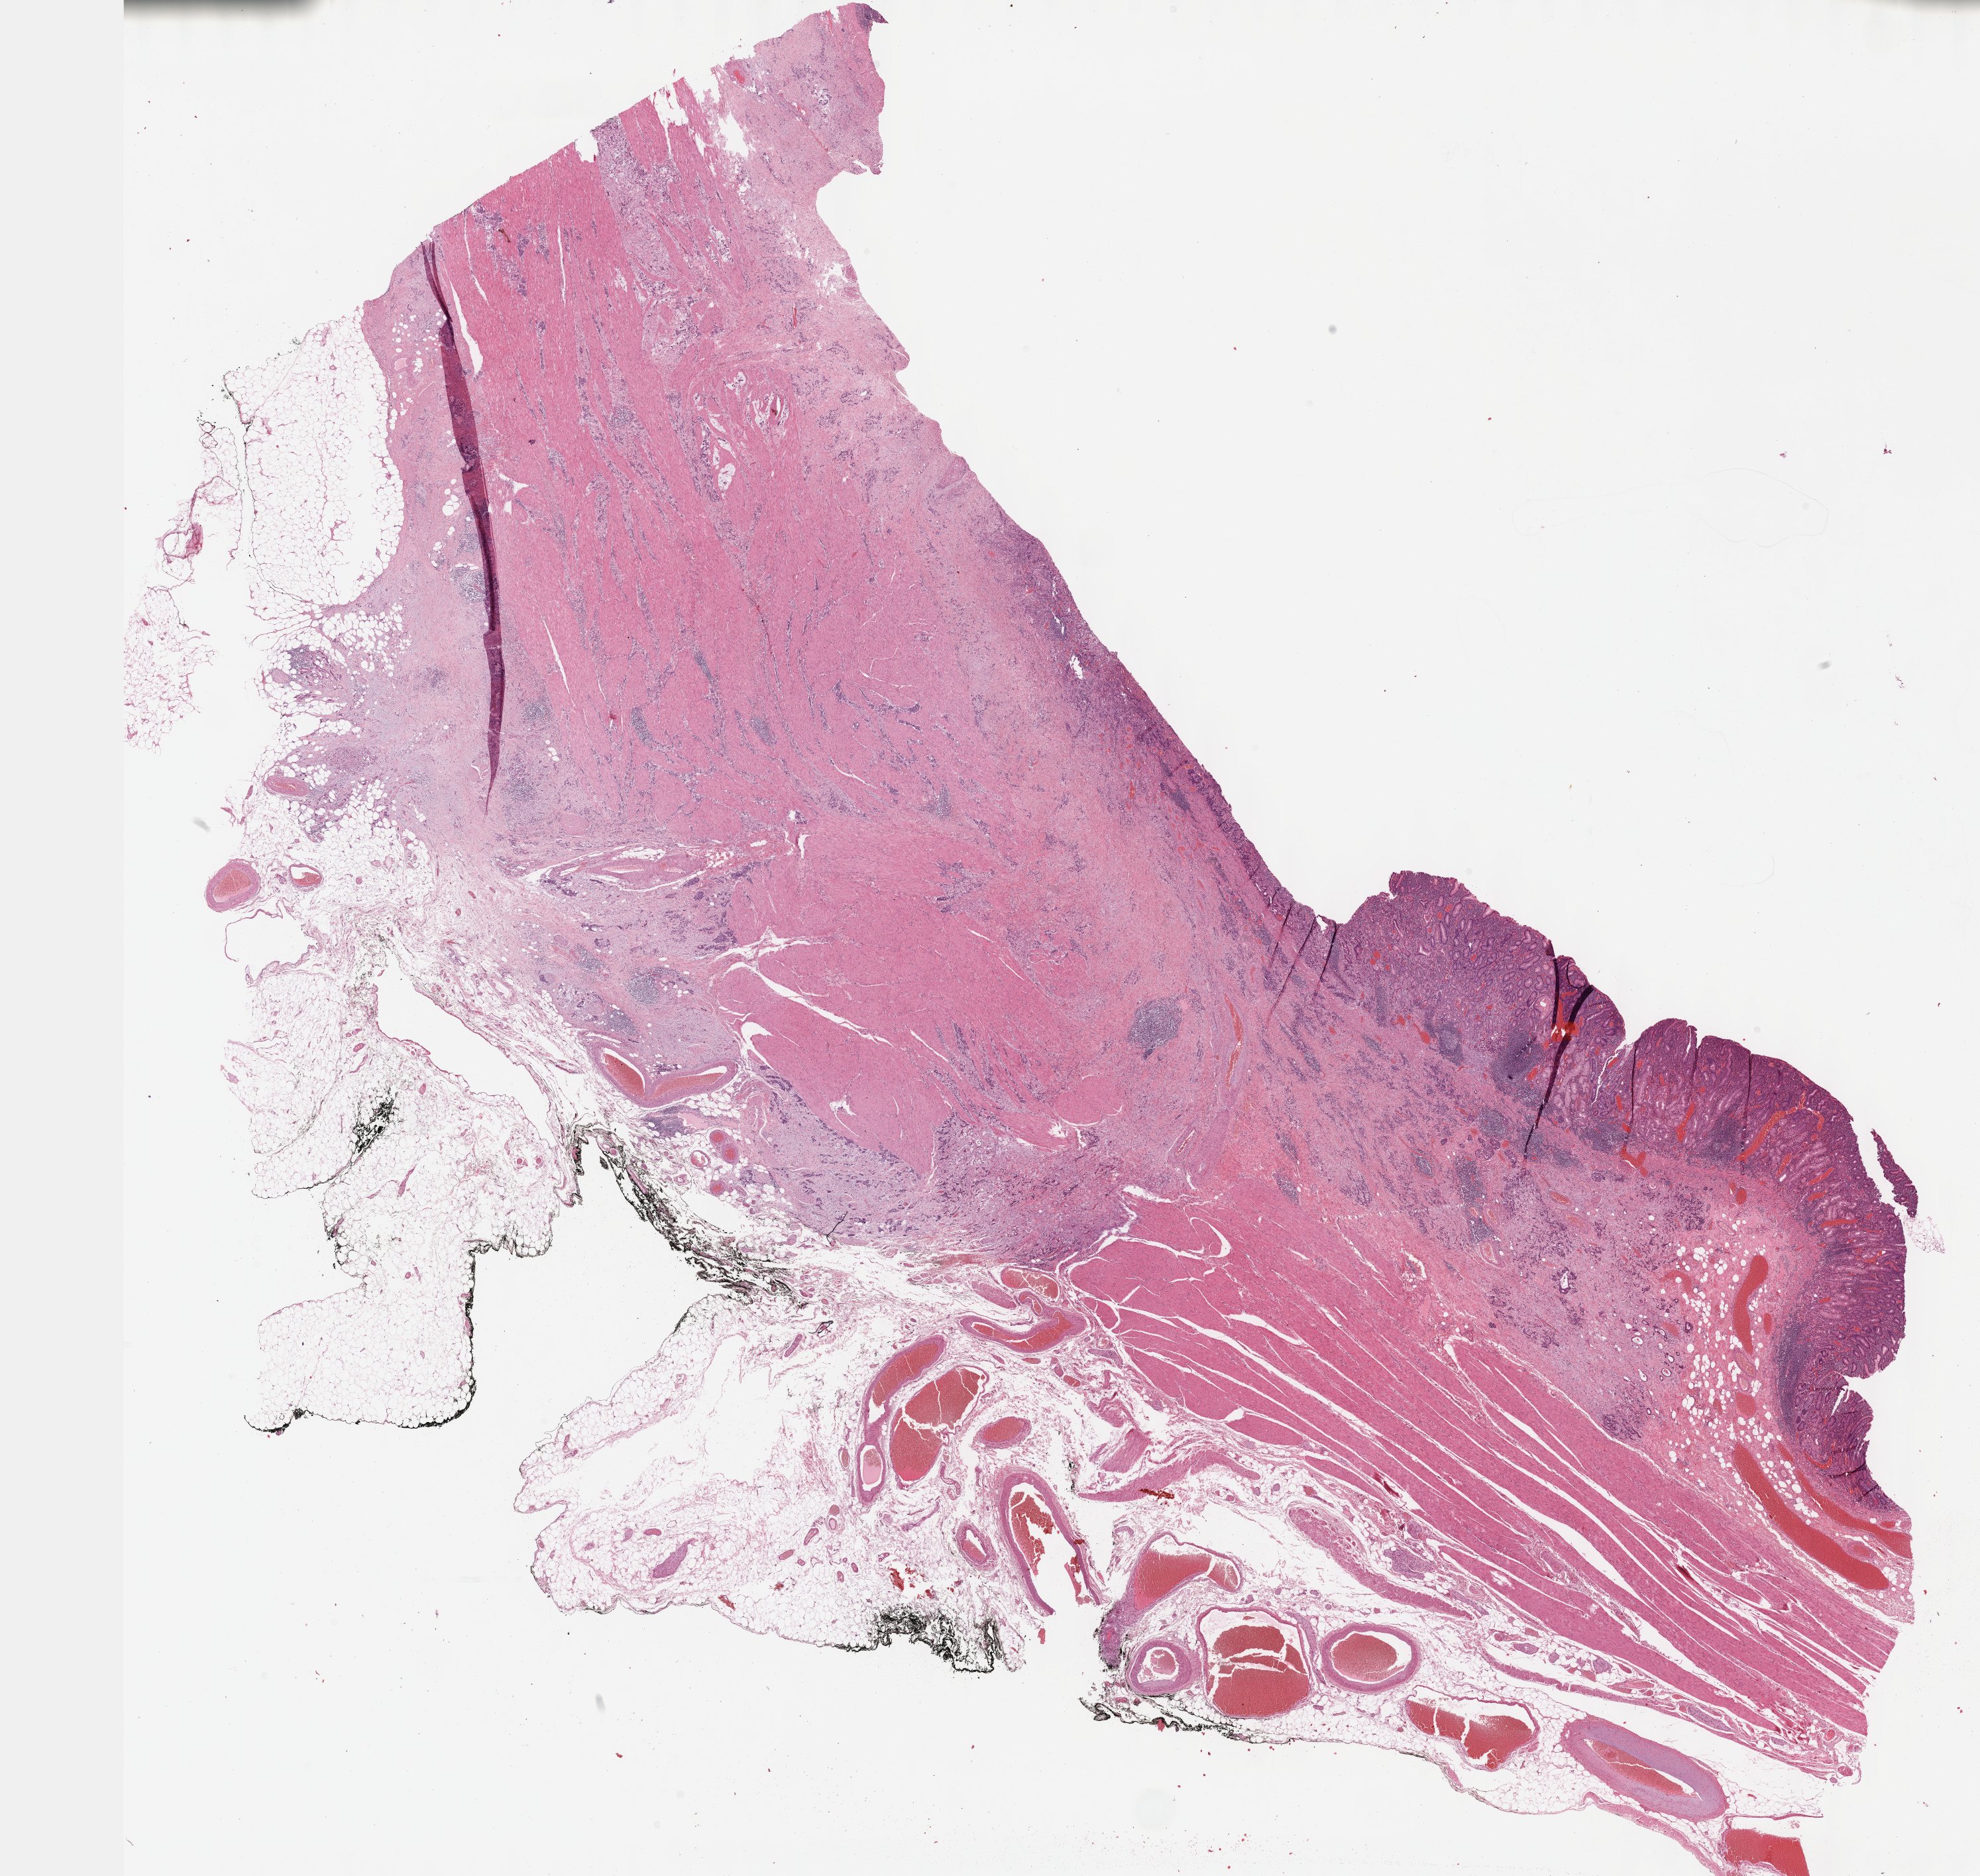
Hematoxylin and eosin (H&E) stained whole-slide image — shown as a low-resolution overview of the whole scanned area (about 24.1 x 22.9 mm, acquisition: 40x scan). Formalin-fixed paraffin-embedded (FFPE) diagnostic section. Primary tumour sample from the stomach. Female patient; age at initial diagnosis 72 years. Histologic grade: G2 (moderately differentiated).
- histologic diagnosis: Adenocarcinoma, intestinal type
- AJCC pathologic stage: IIB
- lymph nodes positive (case pathology): 0 of 19 examined